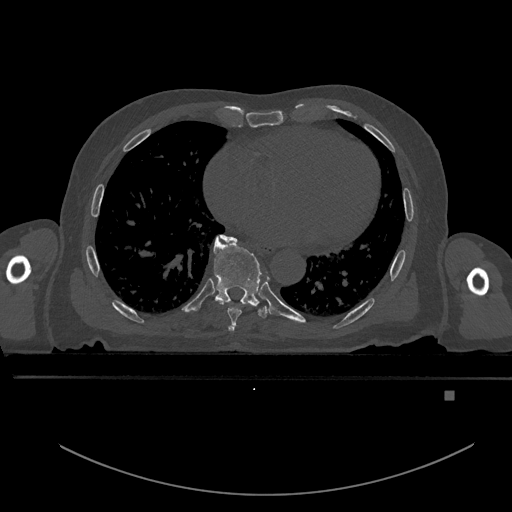
CT including the spine, one axial slice. Slice 224 of 969 in the series (ordered by position). Bone window (W 1800 / L 400 HU). 0.5 mm slice thickness. 512 × 512 image matrix, field of view 456 × 456 mm. Patient: male, 82 years. Case-level facts recorded for this patient, not image findings: primary cancer: prostate.
Outlined on this slice (semi-automatically segmented with operator editing):
- T6 vertebra: bounding box [x1, y1, x2, y2] px = [228, 326, 233, 333]
- T7 vertebra: [221, 235, 242, 326]
- T8 vertebra: [213, 236, 269, 318]